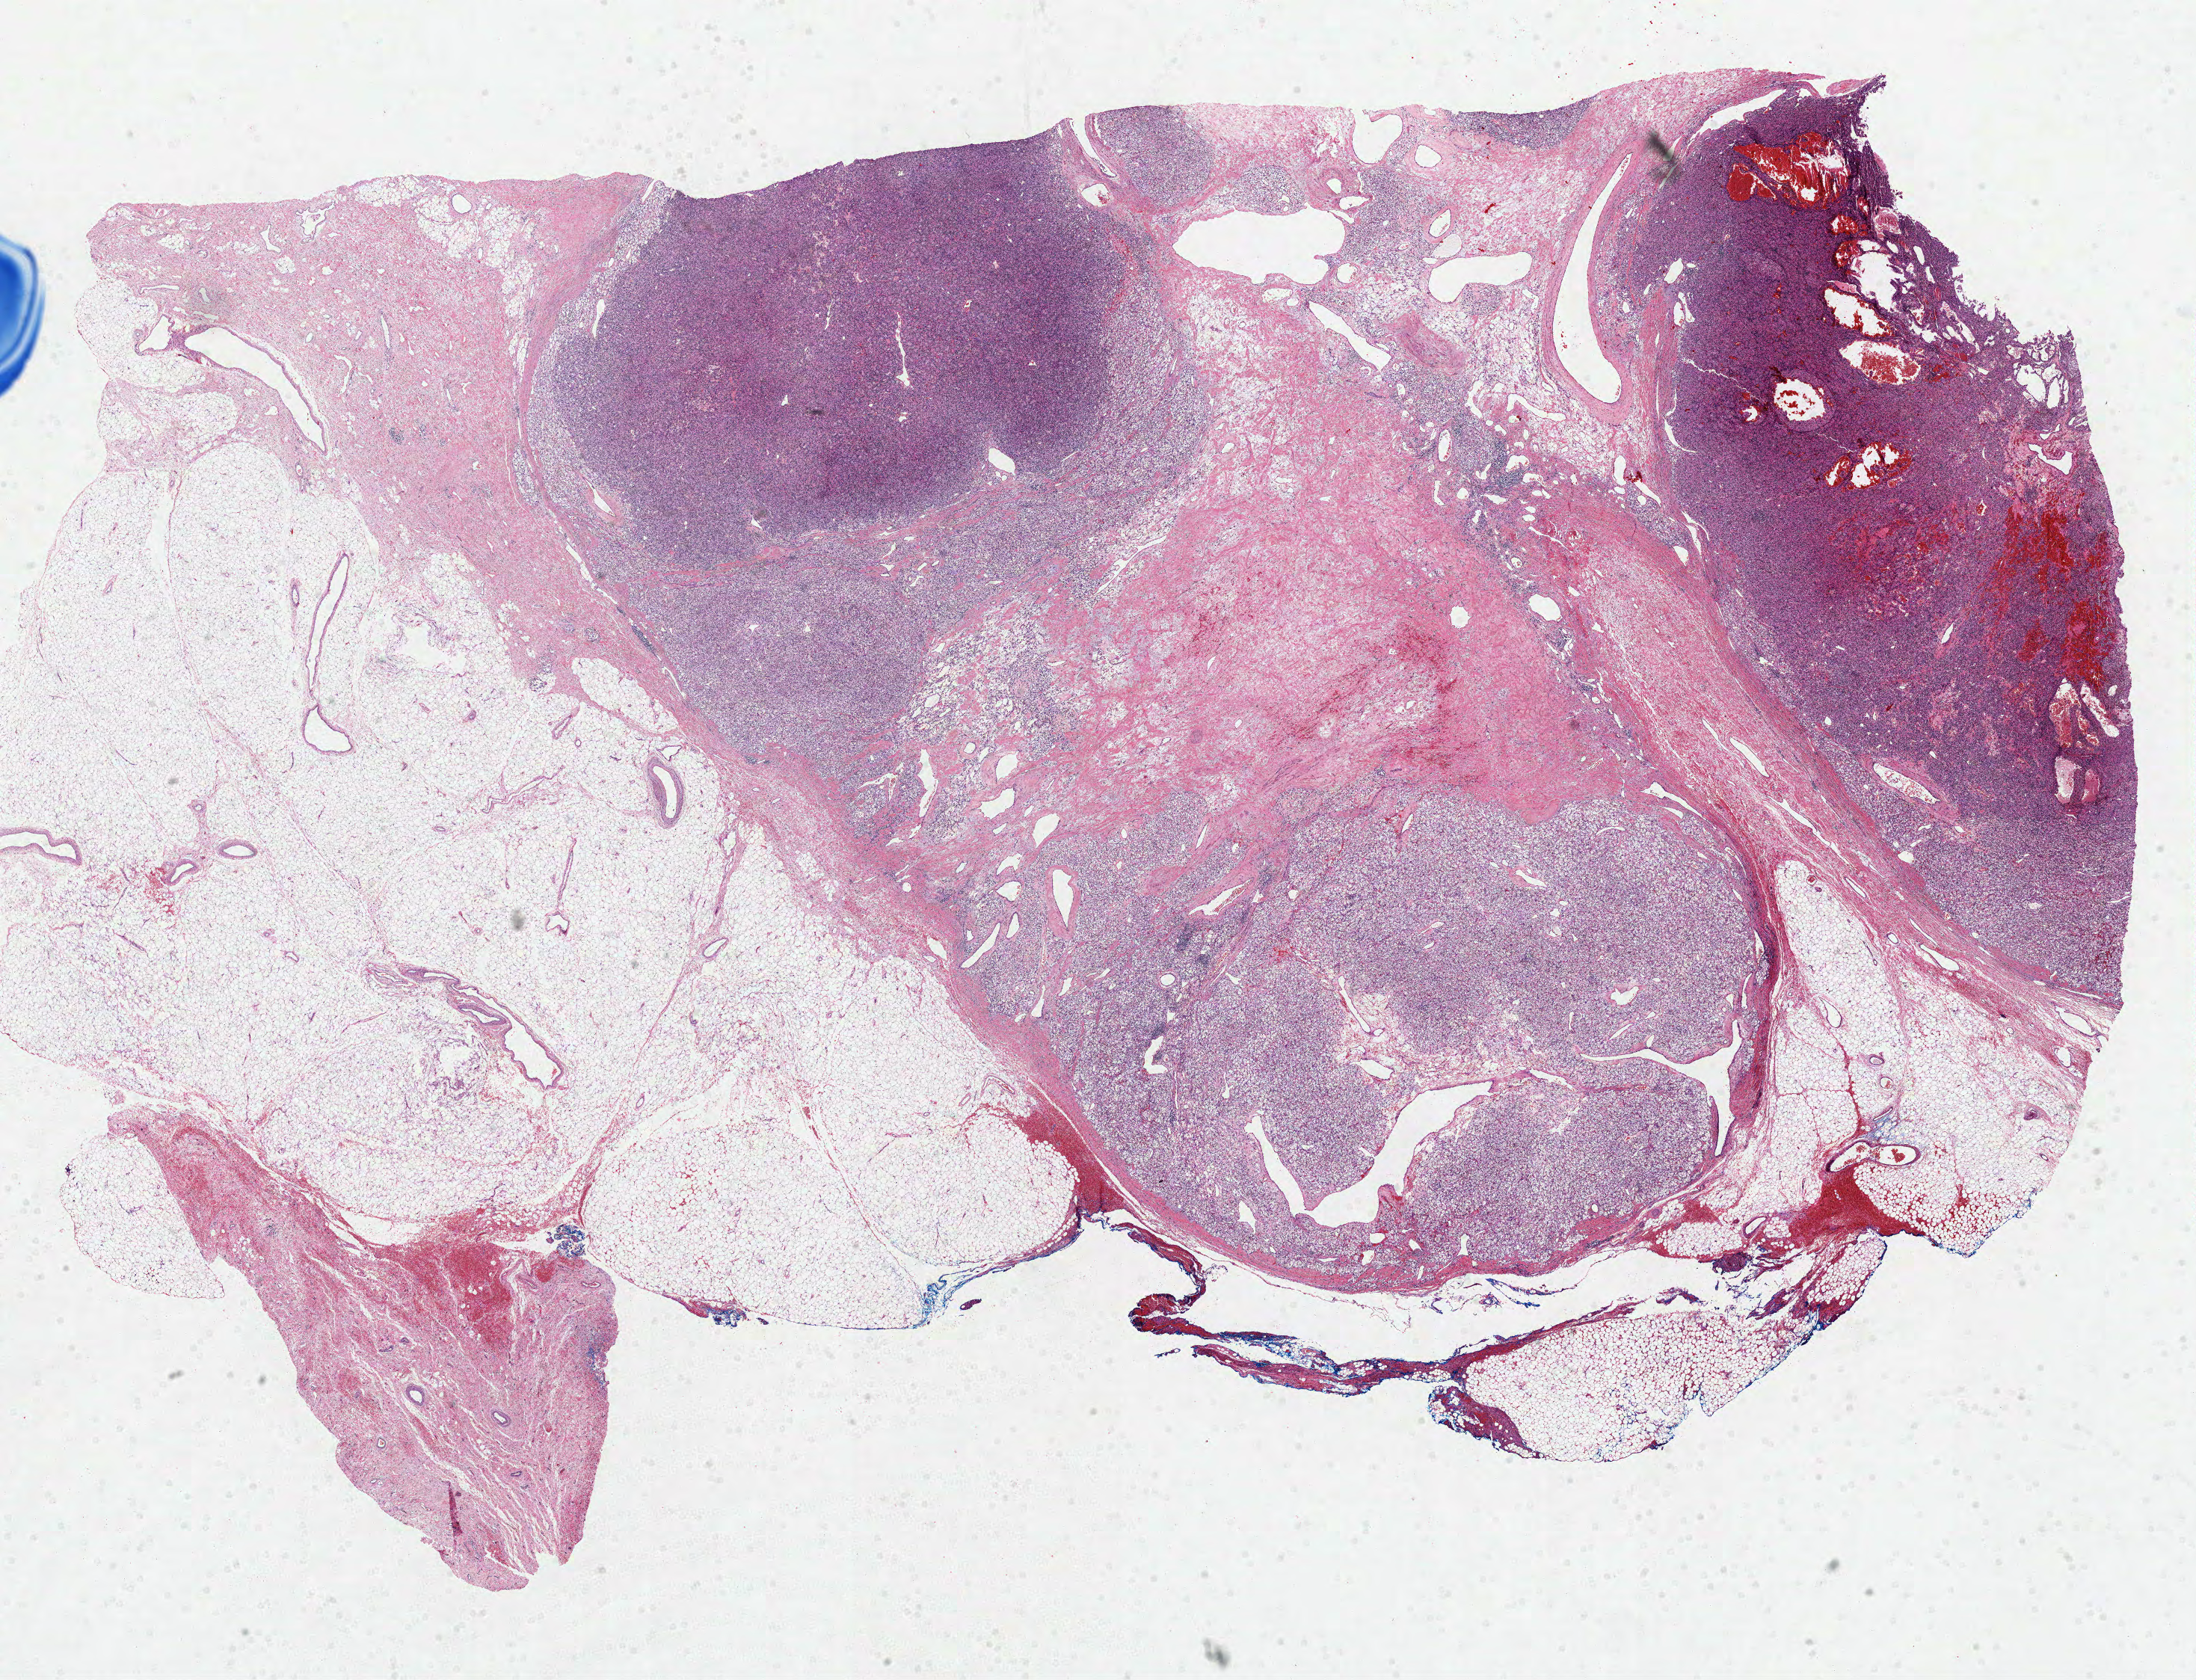
H&E-stained whole-slide image — a low-resolution overview of the entire scanned area, about 23.7 x 18.1 mm. Formalin-fixed paraffin-embedded (FFPE) diagnostic section. Primary tumour sample from the kidney. Patient: female, age at initial diagnosis 69 years. Histologic grade: G2 (moderately differentiated).
AJCC pathologic stage: III. Pathologic diagnosis: Clear cell adenocarcinoma, NOS.